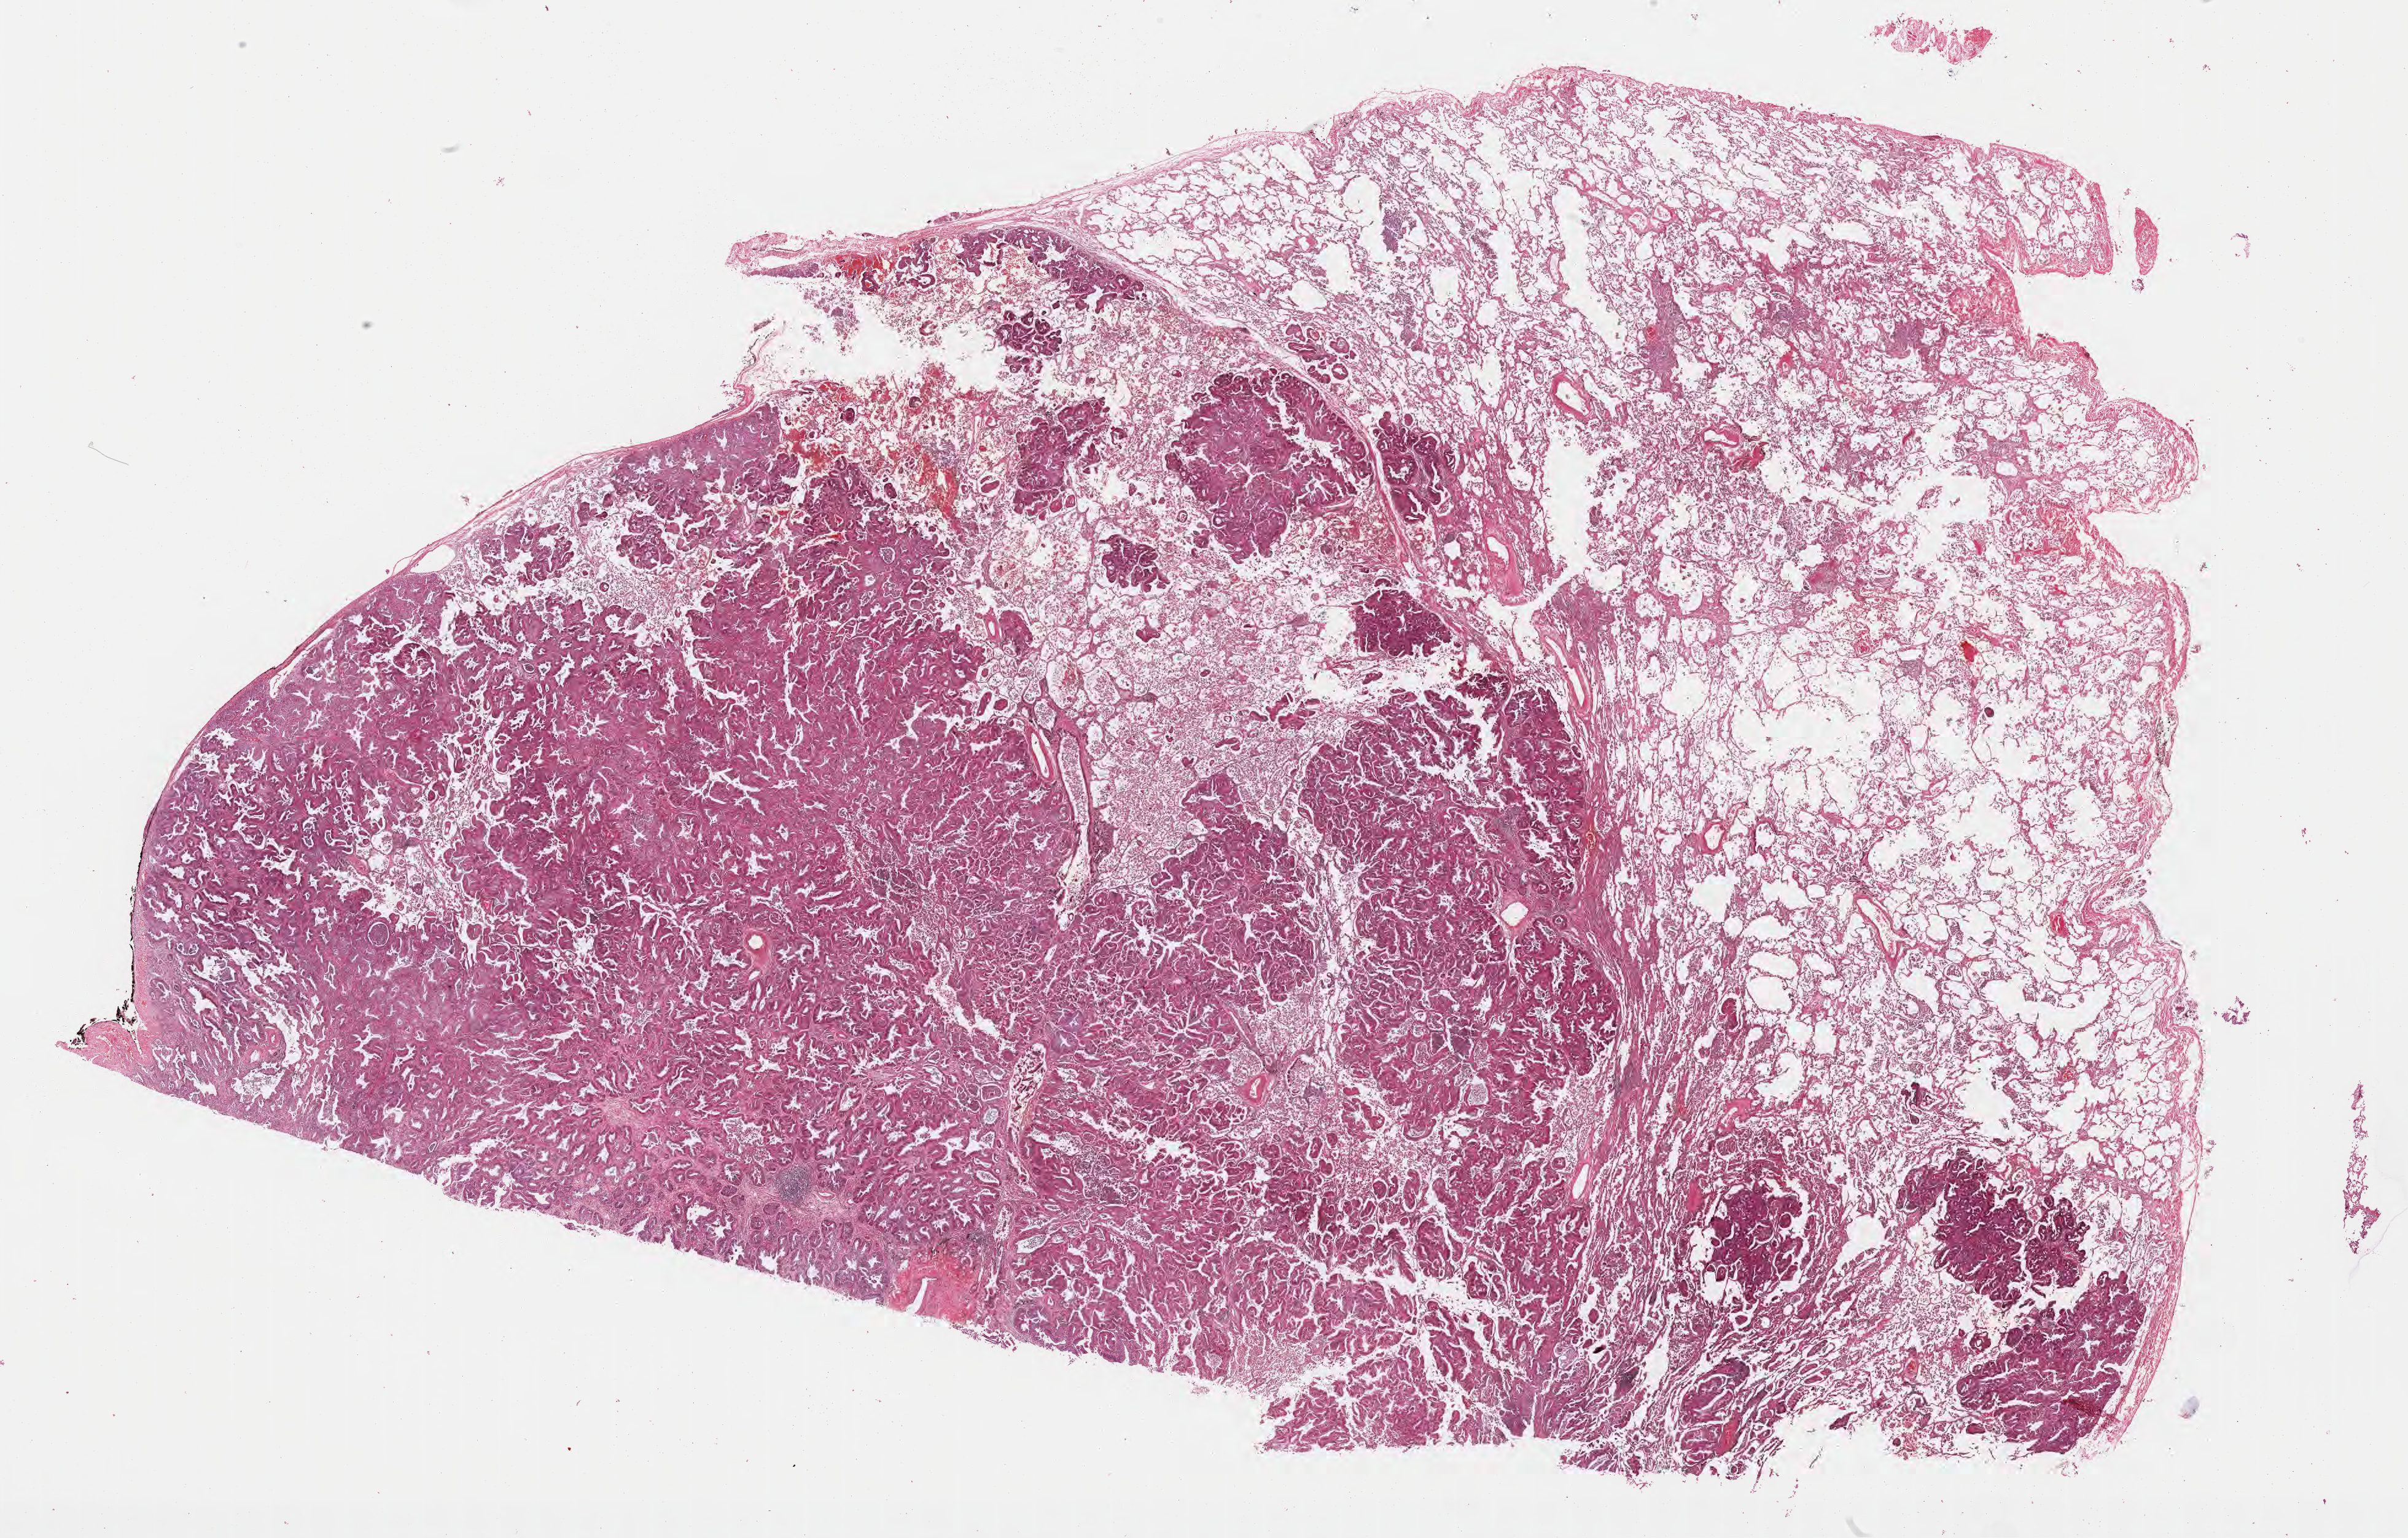
Digitized H&E-stained section, a low-resolution overview of the entire scanned area, about 31.7 x 20.3 mm; formalin-fixed, paraffin-embedded (FFPE) tissue; specimen: primary tumor; site: lower lobe of left lung. Patient: female, aged 70. Slide review estimates, as recorded: tumor cells 70%, tumor nuclei 70%, stromal cells 24%, necrosis 1%, normal cells 5%. Inflammatory infiltration, as recorded: lymphocyte infiltration 2%, monocyte infiltration 7%, neutrophil infiltration 6%.
Diagnosis: Acinar cell carcinoma. AJCC pathologic stage: Stage IB.